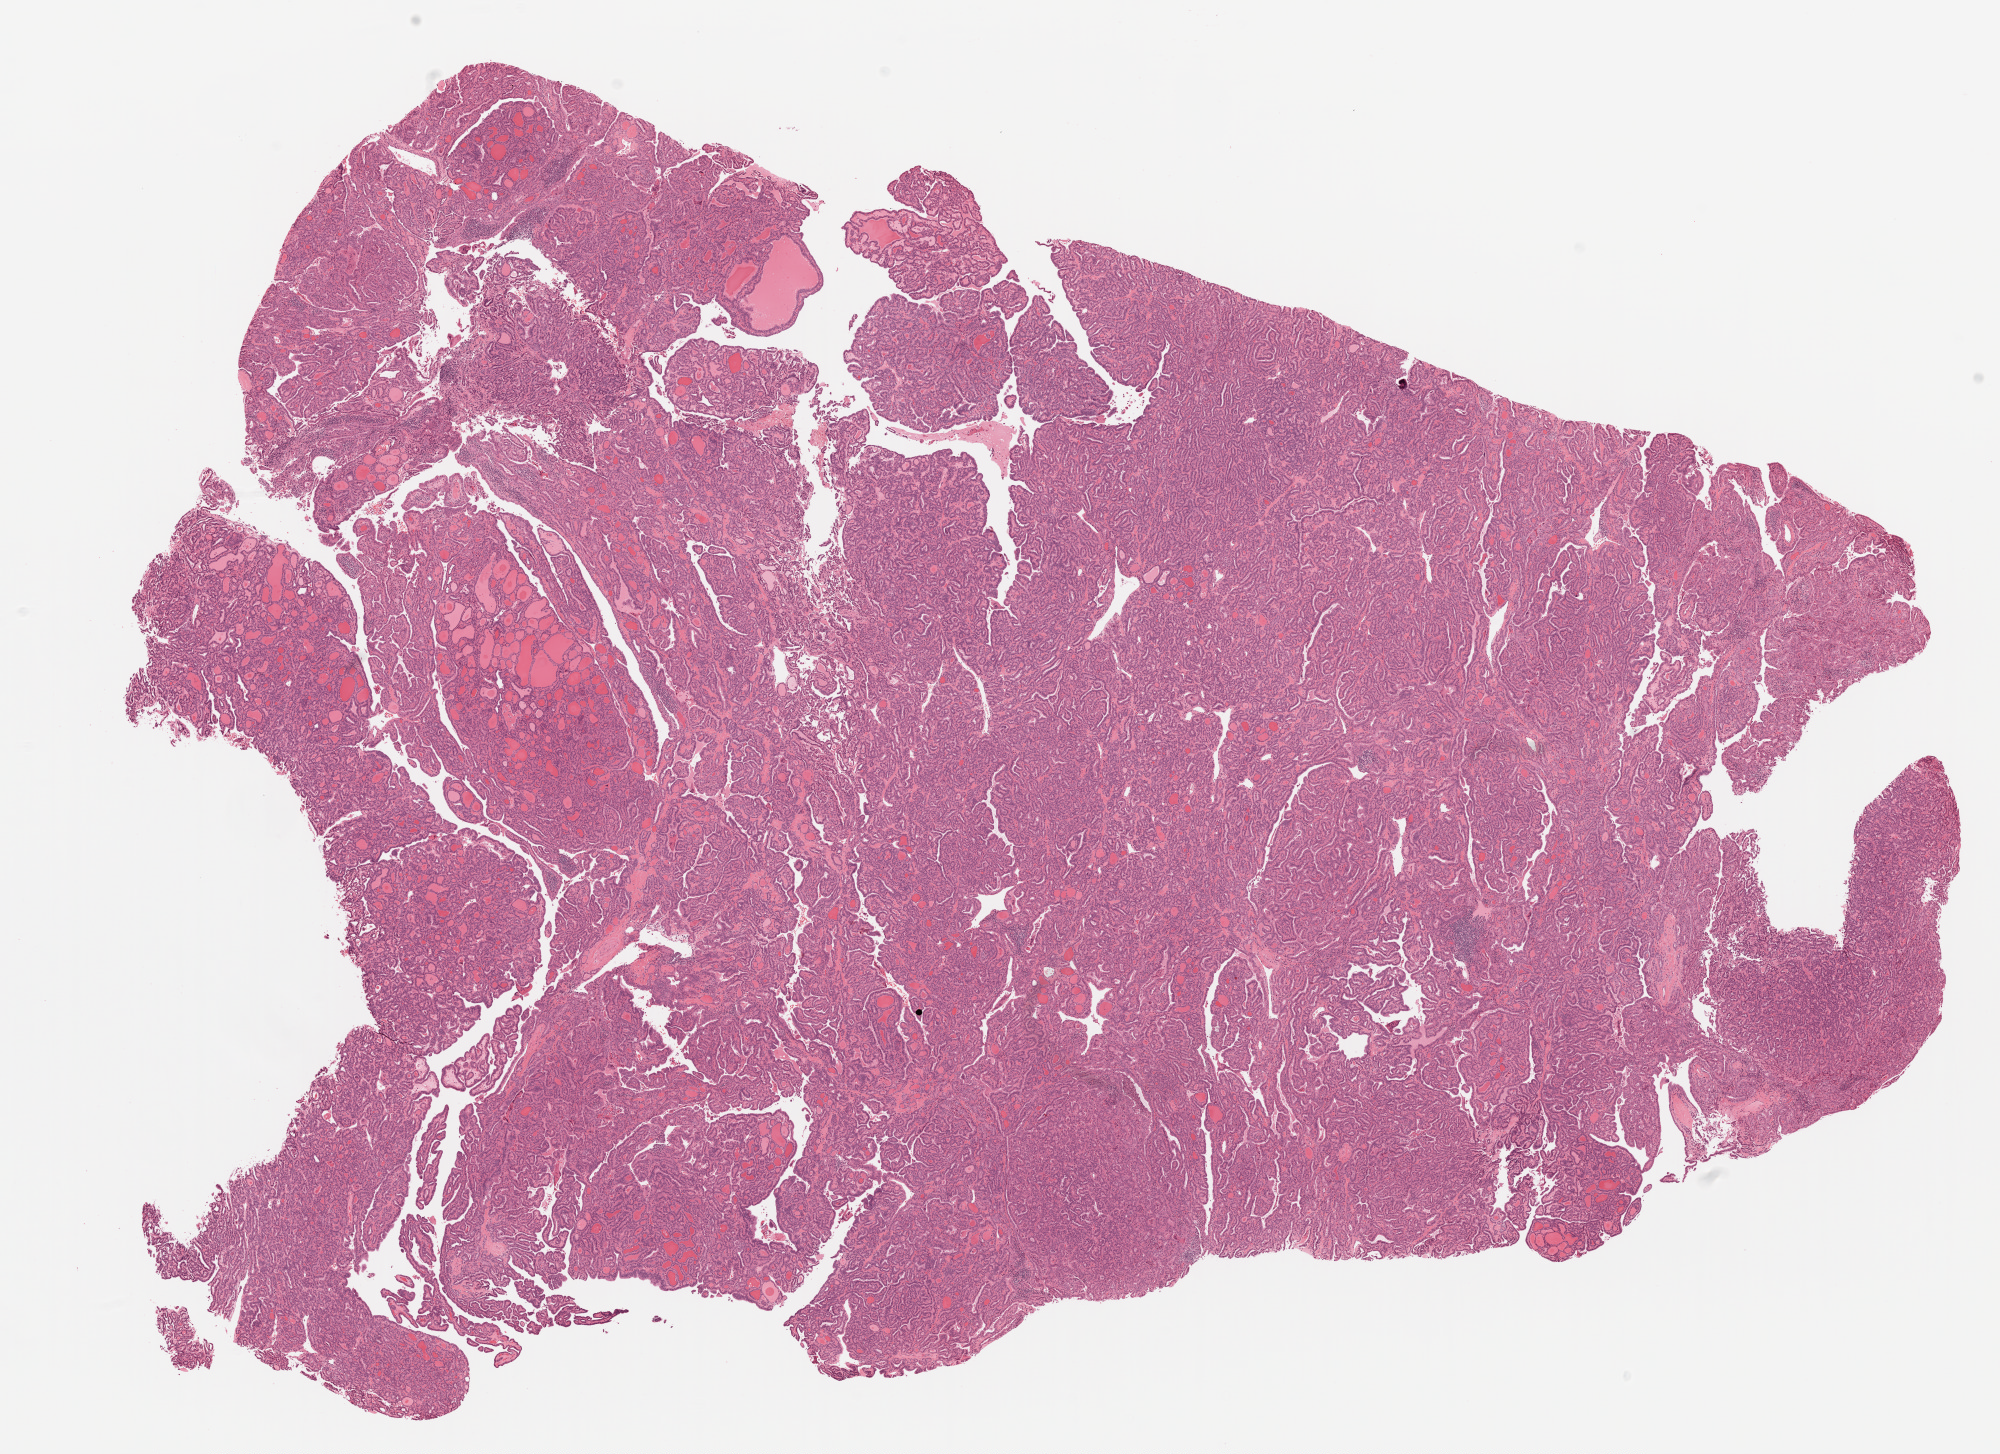
Digitized H&E-stained tissue section (whole slide) — low-resolution overview of the scanned area, about 16.0 x 11.7 mm (from a 20x scan), formalin-fixed paraffin-embedded (FFPE) diagnostic section, primary tumour sample from the thyroid. Female, age 43 years at initial diagnosis.
Pathologic diagnosis: Papillary adenocarcinoma, NOS (thyroid gland).